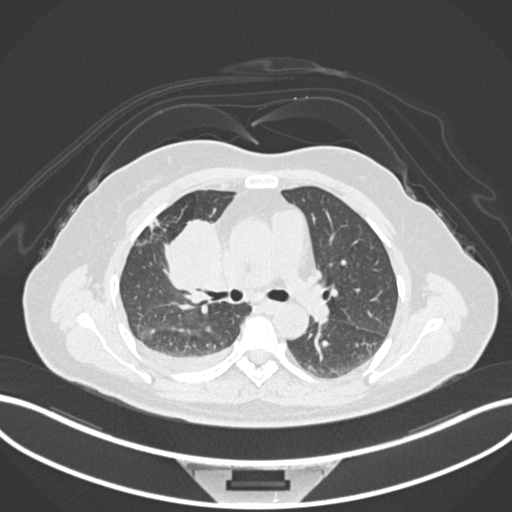
Chest CT, one axial slice. Position 88 of 172 along the scan axis. 120 kVp. Lung window (W 1500 / L -600 HU). 1 mm slice thickness. 512 × 512 image matrix, field of view 400 × 400 mm. Patient: female, 52 years. Case-level facts recorded for this patient, not image findings: clinical TNM (as recorded): T3 N1 M1.
Structures marked on this image (rectangle marked by the reading radiologist):
- lung tumour (recorded histology: adenocarcinoma): bounding box [x1, y1, x2, y2] px = [161, 215, 225, 297]